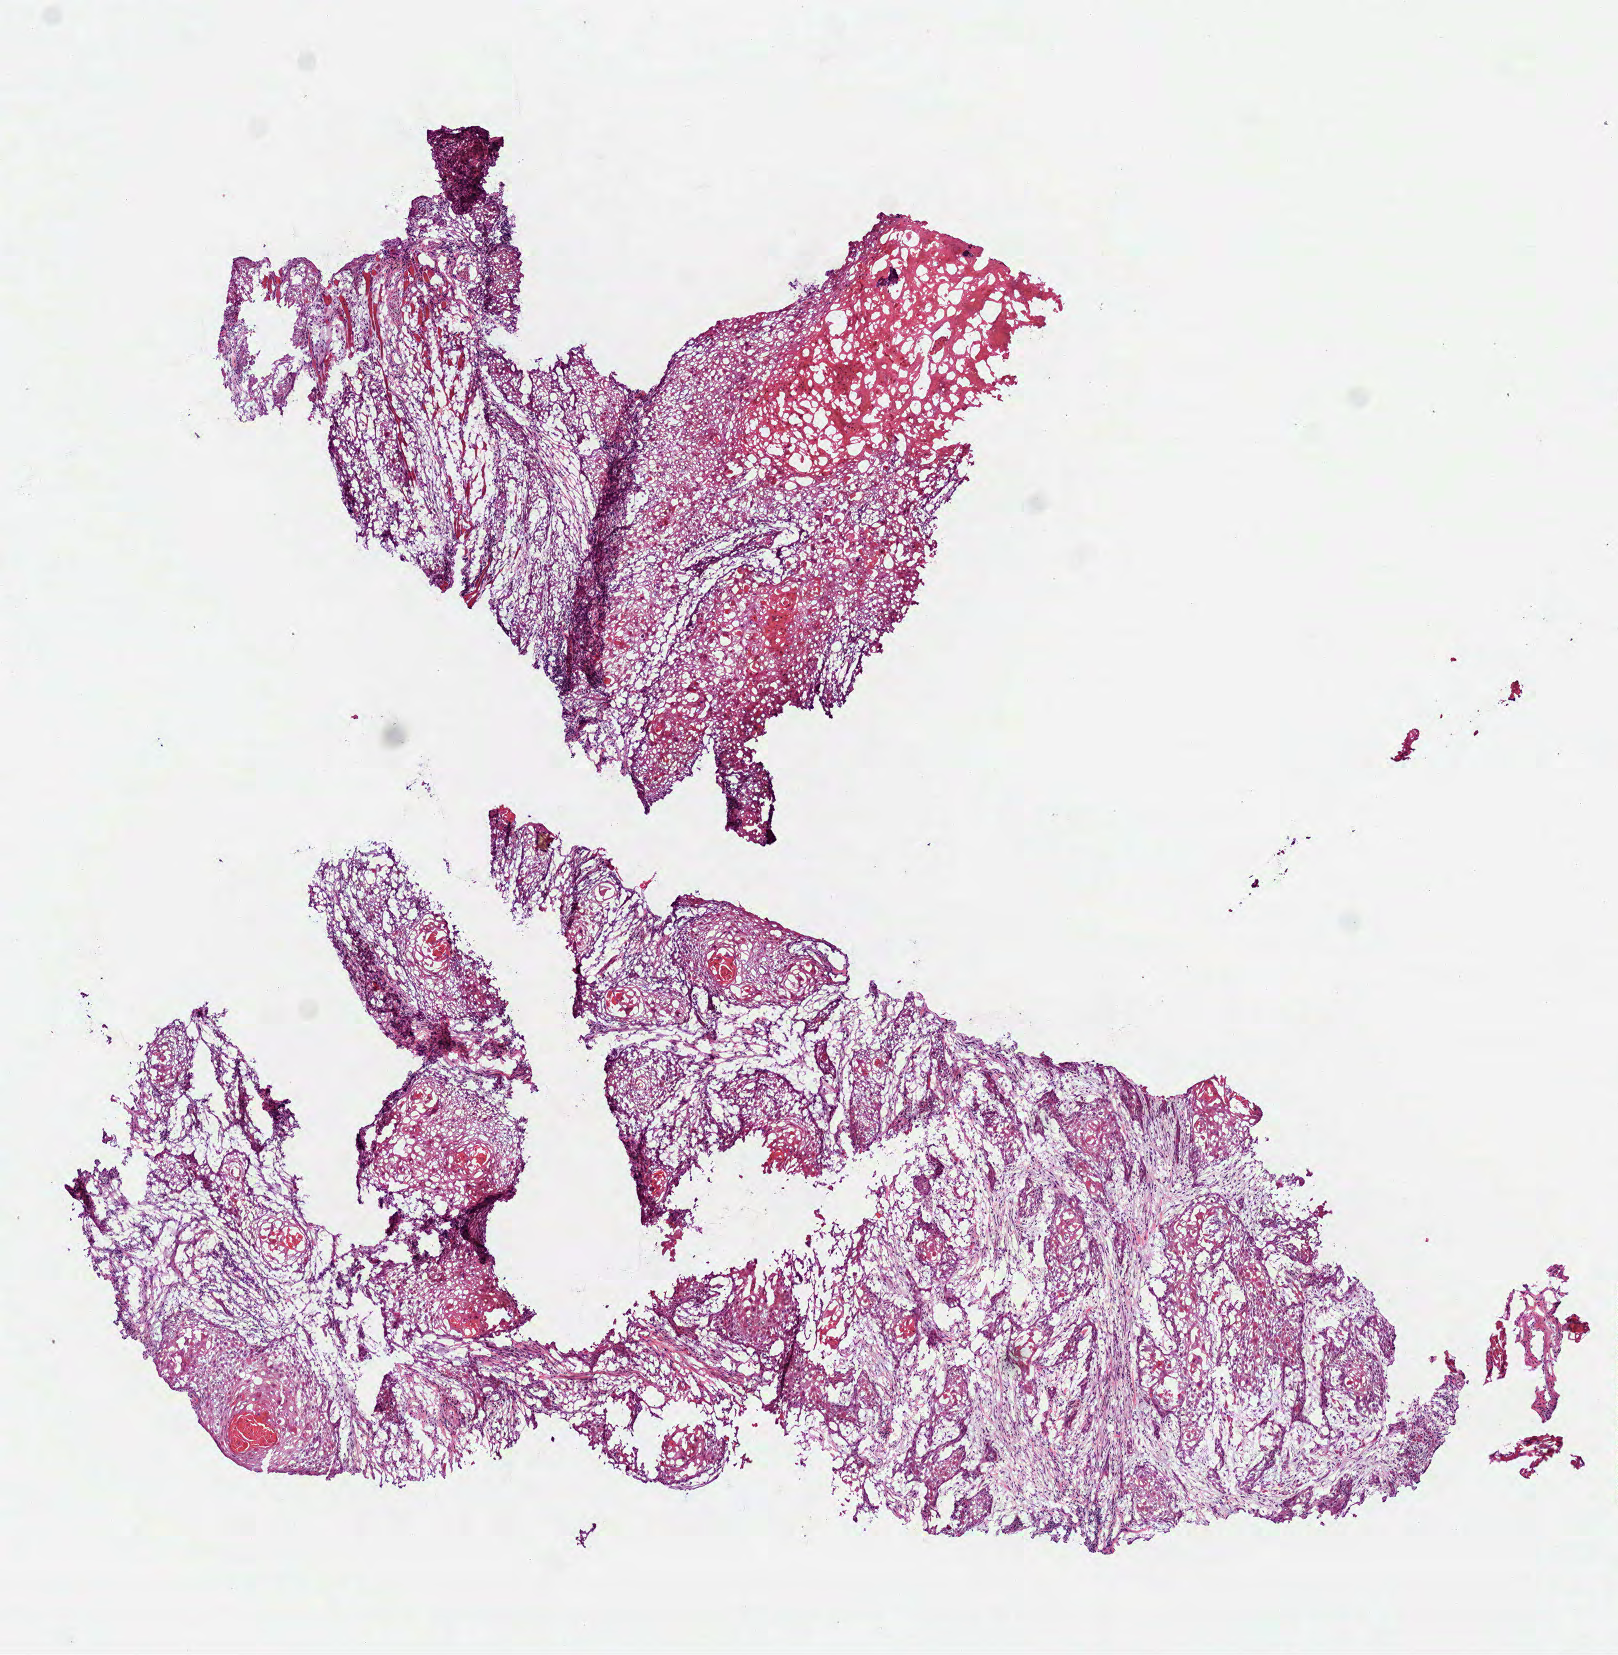
H&E-stained whole-slide image, low-resolution overview of the scanned area, about 6.5 x 6.7 mm (slide scanned at 40x), frozen section from the top of the tissue portion, sample: primary tumour, head and neck. Female patient; age at initial diagnosis 69 years. Histologic grade: G2 (moderately differentiated). Composition of this section per pathologist review: tumour cells 85%, tumour nuclei 75%, normal cells 0%, stromal cells 15%, necrosis 0%.
* histologic diagnosis: Squamous cell carcinoma, NOS (tongue, NOS)
* AJCC pathologic stage: II
* laterality: left